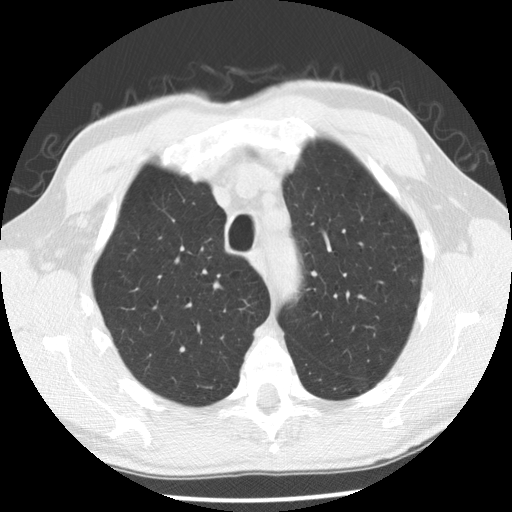
Chest CT (low-dose screening protocol), one axial image. Second screening round (one year after baseline). Lung window (W 1500 / L -600 HU). 2.5 mm slice thickness. Standard (soft-tissue) reconstruction kernel (STANDARD). Slice 36 of 173 in the series. 512 × 512 image matrix, field of view 340 × 340 mm. Male, age 63 years at enrolment. Current smoker at enrolment.
Lesion marked by an expert reader, bounding box [x1, y1, x2, y2] px = [399, 264, 433, 294]. Reader record for this screening exam (exam-level; its link to the box is not recorded): non-calcified nodule or mass ≥4 mm, left upper lobe, 5 × 3 mm, poorly defined margins, soft tissue attenuation, pre-existing on the prior screen: yes; interval growth: no. Official screen result: positive, no significant change: stable abnormalities potentially related to lung cancer, unchanged since the prior screening exam. Lung cancer was diagnosed 445 days after this screen: adenocarcinoma, NOS, left upper lobe, well differentiated (G1), stage IB (AJCC 6th edition), 5 mm at pathology.